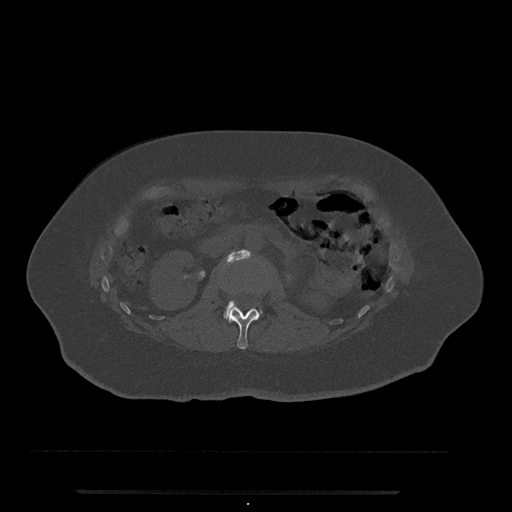
CT including the spine, one axial slice. Slice 75 of 797 in the series (ordered by position). 120 kVp. Bone window (W 1800 / L 400 HU). 0.5 mm slice thickness. 512 × 512 image matrix, field of view 440 × 440 mm. Female patient, age 51 years. From the clinical record (not read from this slice): primary cancer: neuro; vertebrae with lytic lesions (as recorded): T8.
Outlined on this slice (semi-automatic segmentation, software-assisted and operator-edited):
- L1 vertebra: bounding box (x1, y1, x2, y2) in pixels: (224, 307, 261, 349)
- L2 vertebra: (225, 250, 263, 315)